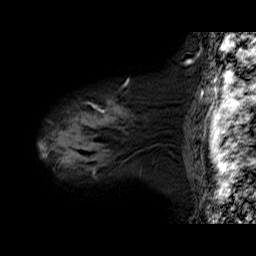
Breast MRI (dynamic contrast-enhanced), one sagittal slice; slice 54 of 60 in the series (ordered by position); dynamic contrast-enhanced series, time point 2 of 6 at this slice position (early post-contrast); 1.5 T; TE 6.3 ms, TR 32.9 ms; 4 mm slice thickness; 256 × 256 image matrix, field of view 200 × 200 mm. Female patient. Case-level facts recorded for this patient, not image findings: setting: breast cancer imaged before/during neoadjuvant chemotherapy; receptor status: HER2-positive.
Annotated regions visible in this slice (semi-automatically segmented with operator editing):
- analysis volume of interest (the breast-tissue region the enhancement analysis was run in; not a lesion): bounding box [x1, y1, x2, y2] px = [43, 81, 171, 175]
- tumour enhancement mask (voxels above the 100 % enhancement threshold inside the analysis volume of interest): [43, 112, 110, 157]